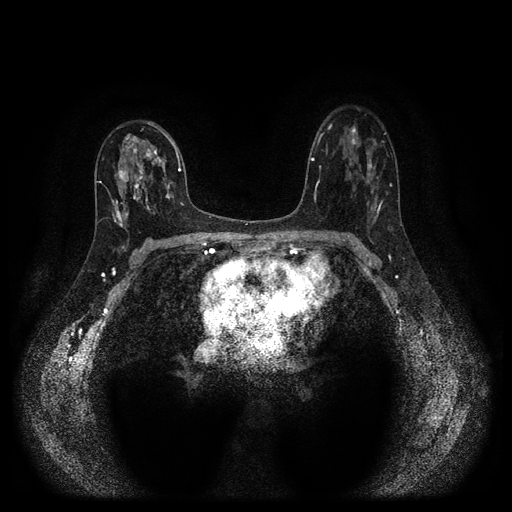
Breast MRI (dynamic contrast-enhanced, multi-phase), one axial slice. Slice 63 of 116 in the series (ordered by position). Dynamic contrast-enhanced series, time point 2 of 5 at this slice position (early post-contrast). 1.5 T. TE 2.7 ms, TR 5.4 ms. 2 mm slice thickness. 512 × 512 image matrix, field of view 330 × 330 mm. Female patient, age 47 years.
Structures marked on this image (semi-automatically segmented with operator editing):
- breast lesion (labelled 'tumour' in the annotation; benign lesions carry a separate 'benign' label): box from (x=113, y=133) to (x=184, y=222) px